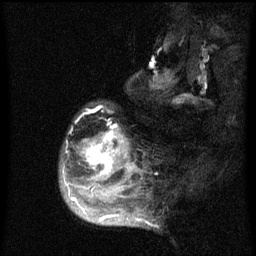
Breast MRI (dynamic contrast-enhanced), one sagittal slice; position 15 of 60 along the scan axis; dynamic contrast-enhanced series, image 2 of 3 at this slice position (ordered by acquisition); 1.5 T; TE 4.2 ms, TR 8 ms; 2 mm slice thickness; 256 × 256 image matrix. Female patient, age 50 years.
Outlined on this slice (semi-automatically segmented with operator editing):
- analysis volume of interest (the breast-tissue region the enhancement analysis was run in; not a lesion): bounding box <60,106,142,216> (left, top, right, bottom; pixels)
- tumour enhancement mask (voxels above the 70 % enhancement threshold inside the analysis volume of interest): <66,130,127,216>